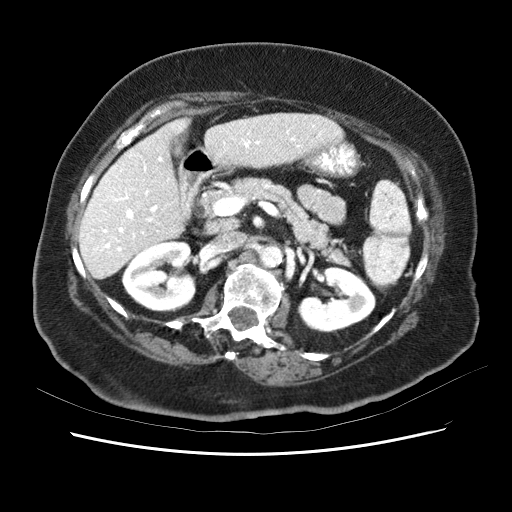
Contrast-enhanced abdominal CT (liver protocol), one axial slice; slice 25 of 62 in the series (ordered by position); reconstruction kernel STANDARD; soft-tissue window (W 400 / L 40 HU); 2.5 mm slice thickness; 512 × 512 image matrix, field of view 340 × 340 mm. Case-level facts recorded for this patient, not image findings: diagnosis: hepatocellular carcinoma (patient treated with transarterial chemoembolisation; whether this scan precedes or follows treatment is not stated here); TNM stage (as recorded): Stage-I; Child-Pugh class: B; tumour nodularity: uninodular; tumour size: 5.3 cm.
Annotated regions visible in this slice (semi-automatic segmentation, software-assisted and operator-edited):
- liver parenchyma outside the tumour (the mass and vessels are separate outlines, so this box may not span the whole liver): bounding box <78,112,348,280> (left, top, right, bottom; pixels)
- liver vessels: <81,127,331,262>